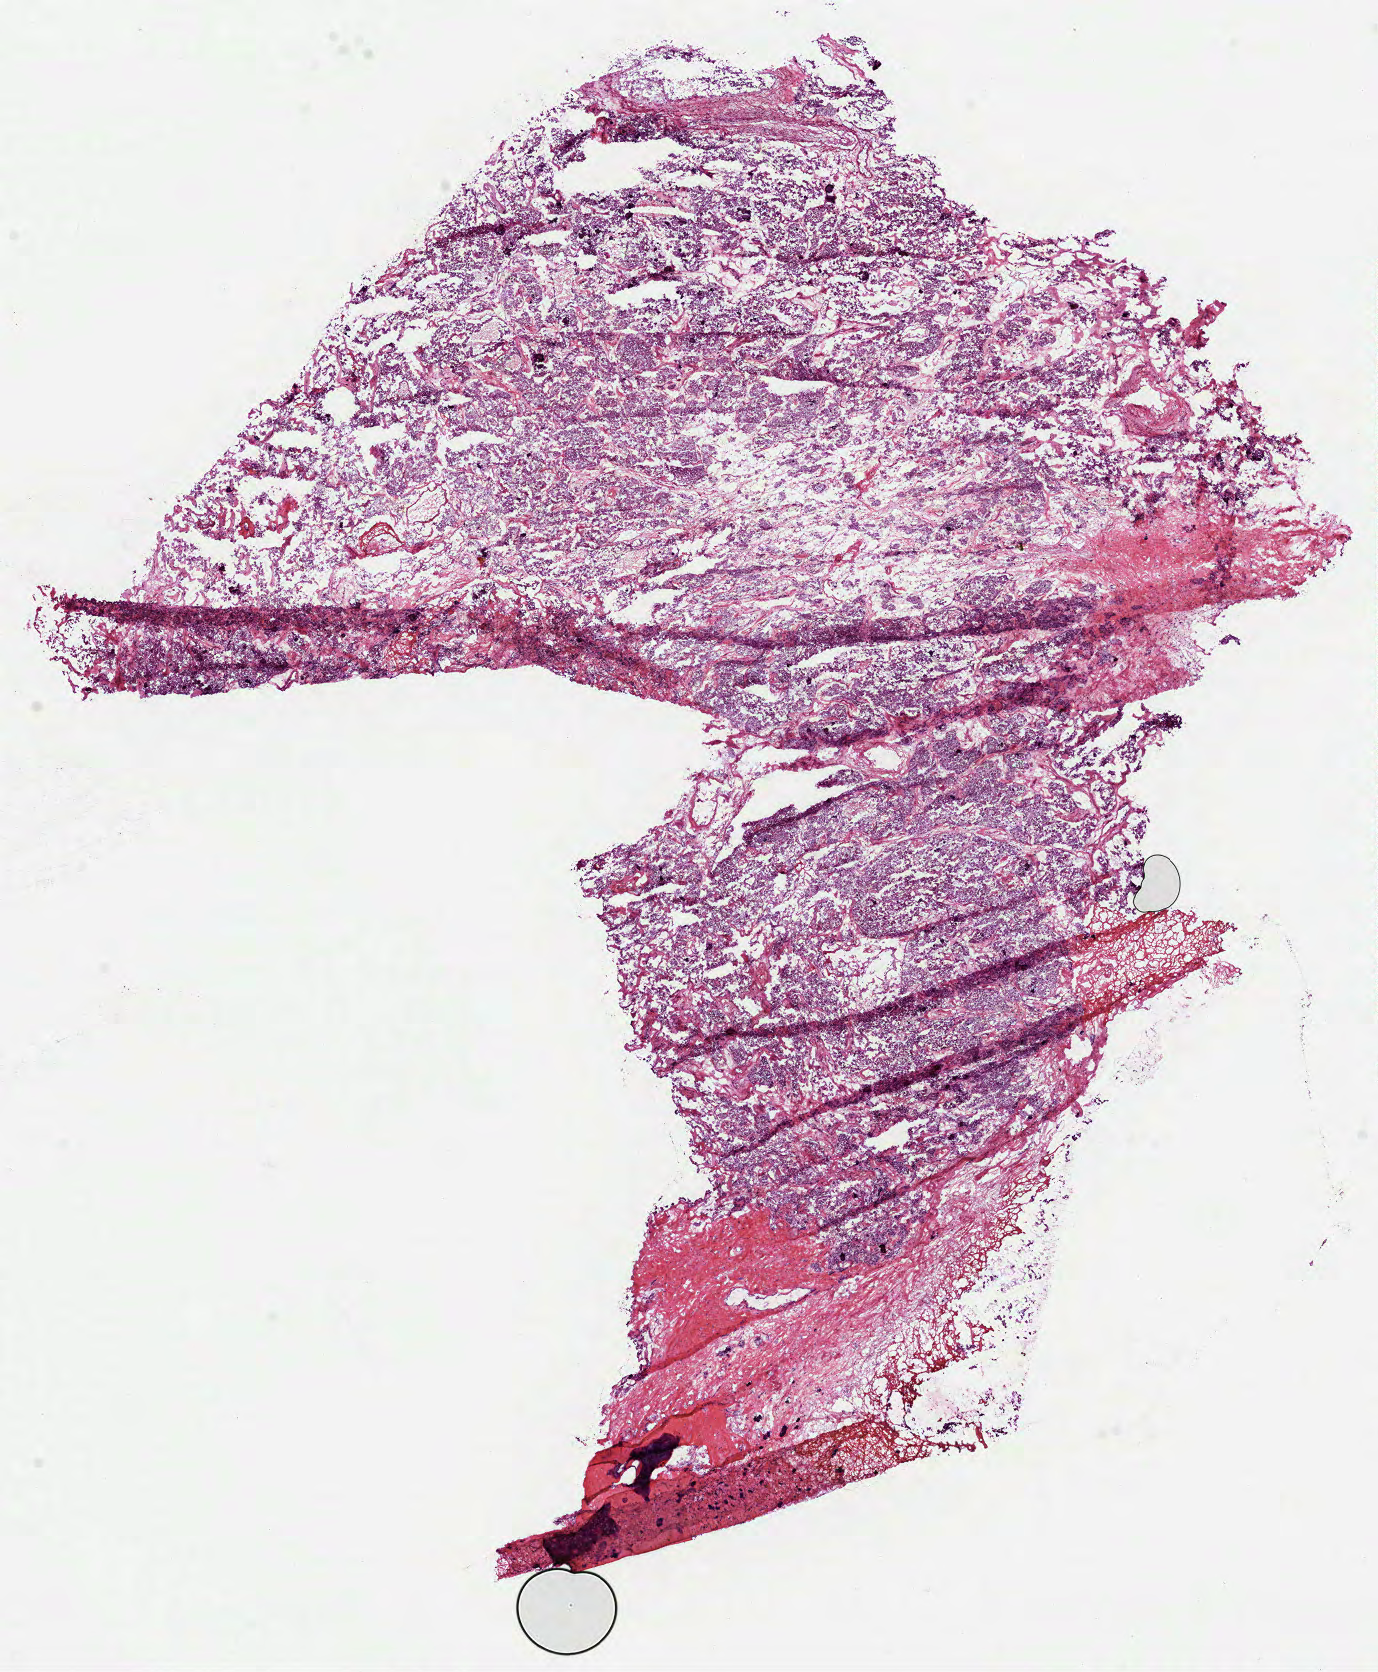
Digitized Hematoxylin and eosin (H&E) stained tissue section (whole slide), shown as a low-resolution overview of the whole scanned area (about 11.1 x 13.5 mm, from a 40x scan); frozen section from the top of the tissue portion; kidney, primary tumour sample. Male, age 49 years at initial diagnosis. Pathologist review of this section (percent, as recorded): tumour cells 35%, tumour nuclei 60%, normal cells 0%, stromal cells 55%, necrosis 10%. Inflammatory infiltration, as recorded: lymphocyte infiltration 4%, monocyte infiltration 0%, neutrophil infiltration 0%.
Histologic diagnosis: Renal cell carcinoma, chromophobe type. AJCC pathologic stage: II (7th edition). TNM: T2a NX MX.